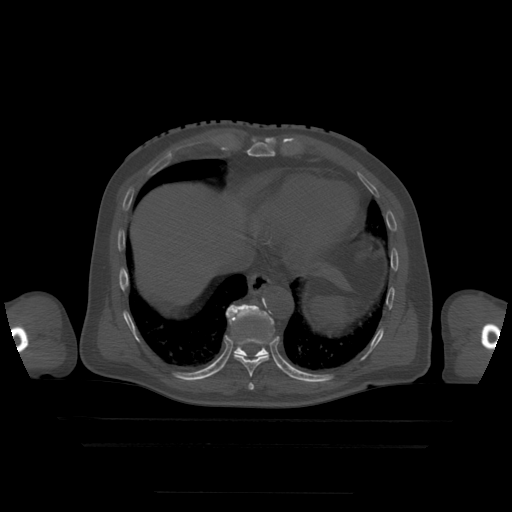
CT including the spine, one axial slice; position 254 of 522 along the scan axis; bone window (W 1800 / L 400 HU); 1.25 mm slice thickness; 512 × 512 image matrix, field of view 436 × 436 mm. Patient age 68 years. Case-level facts recorded for this patient, not image findings: primary cancer: urothelial.
Annotated regions visible in this slice (semi-automatically segmented with operator editing):
- T10 vertebra: bounding box [x1, y1, x2, y2] px = [226, 304, 274, 357]
- T8 vertebra: [250, 384, 254, 390]
- T9 vertebra: [230, 309, 274, 390]